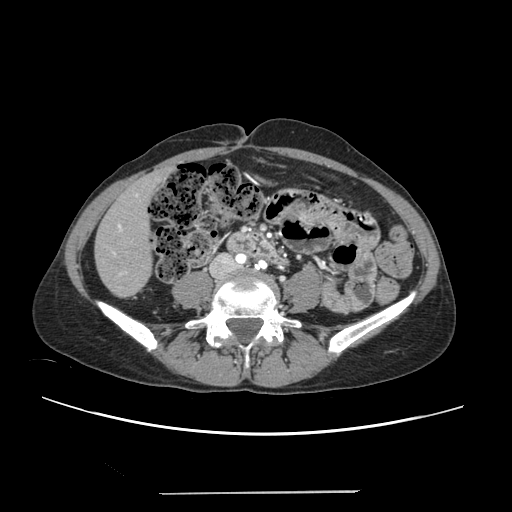
Contrast-enhanced abdominal CT, one axial slice. Position 43 of 240 along the scan axis. 120 kVp. Intravenous contrast given. Soft-tissue window (W 400 / L 40 HU). 512 × 512 image matrix, field of view 371 × 371 mm. Female patient, age 60 years. From the clinical record (not read from this slice): diagnosis: colorectal cancer liver metastases, imaged before liver resection; multiple liver metastases: no.
Outlined on this slice (manually delineated by an expert):
- liver: bounding box <96,171,166,296> (left, top, right, bottom; pixels)
- planned liver remnant (the part of the liver to remain after resection): <96,172,165,296>
- portal vein (with intrahepatic branches): <112,194,138,274>